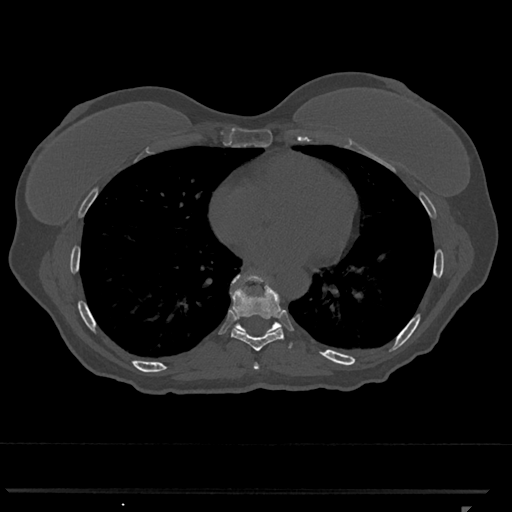
CT including the spine, one axial slice; position 655 of 793 along the scan axis; 120 kVp; bone window (W 1800 / L 400 HU); 512 × 512 image matrix, field of view 380 × 380 mm. Female patient, age 62 years. From the clinical record (not read from this slice): primary cancer: renal.
Outlined on this slice (semi-automatically segmented with operator editing):
- T7 vertebra: bounding box <254,363,259,370> (left, top, right, bottom; pixels)
- T8 vertebra: <231,281,283,351>
- T9 vertebra: <231,273,282,335>